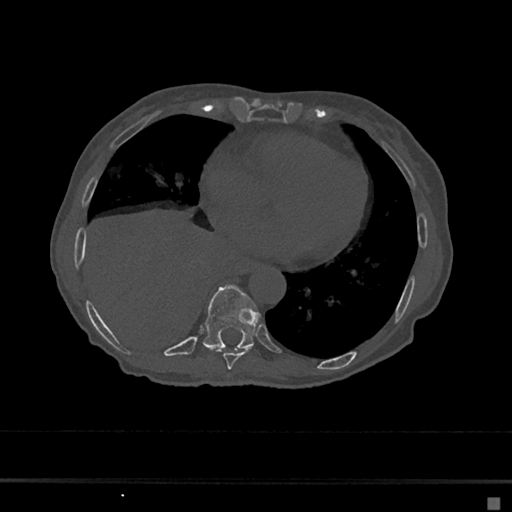
CT including the spine, one axial slice; slice 294 of 797 in the series (ordered by position); reconstruction kernel Br40s/3; 120 kVp; bone window (W 1800 / L 400 HU); 512 × 512 image matrix, field of view 360 × 360 mm. Female patient, age 68 years. Case-level facts recorded for this patient, not image findings: primary cancer: renal.
Outlined on this slice (semi-automatically segmented with operator editing):
- T8 vertebra: bounding box (x1, y1, x2, y2) in pixels: (216, 349, 251, 370)
- T9 vertebra: (203, 285, 260, 351)